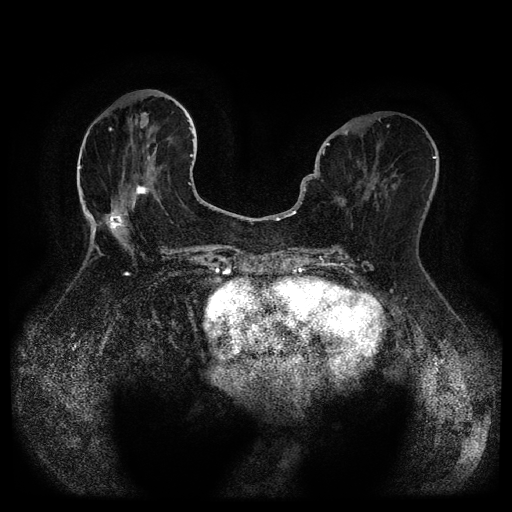
Breast MRI (dynamic contrast-enhanced, multi-phase), one axial slice. Position 40 of 116 along the scan axis. Dynamic contrast-enhanced series, time point 2 of 5 at this slice position (early post-contrast). 1.5 T. TE 2.6 ms, TR 5.3 ms. 2 mm slice thickness. 512 × 512 image matrix. Patient: female, 75 years.
Annotated regions visible in this slice (semi-automatic segmentation, software-assisted and operator-edited):
- breast lesion (labelled benign in the annotation): box from (x=132, y=183) to (x=149, y=198) px
- breast lesion (labelled benign in the annotation): (x=106, y=210)–(x=125, y=234)